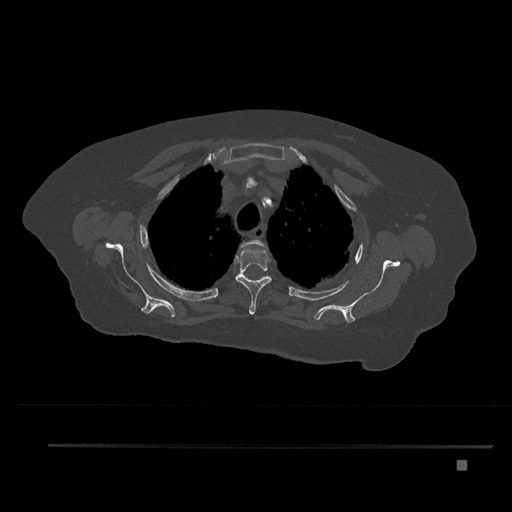
CT including the spine, one axial slice; slice 635 of 797 in the series (ordered by position); 120 kVp; bone window (W 1800 / L 400 HU); 0.5 mm slice thickness; 512 × 512 image matrix, field of view 437 × 437 mm. Female patient, age 76 years. From the clinical record (not read from this slice): primary cancer: lung; vertebrae with lytic lesions (as recorded): T11, L3.
Structures marked on this image (semi-automatic segmentation, software-assisted and operator-edited):
- T2 vertebra: box from (x=241, y=240) to (x=266, y=248) px
- T3 vertebra: (x=235, y=250)–(x=272, y=315)